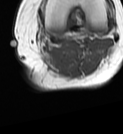
MRI of an extremity soft-tissue mass, one axial slice; position 51 of 68 along the scan axis; MR volume resampled by the dataset authors to the PET/CT grid (not the native acquisition matrix); 123 × 134 image matrix. Female patient. Case-level facts recorded for this patient, not image findings: histological type: extraskeletal high grade osteogenic sarcoma; grade: high; site of the primary tumour: left calf.
Outlined on this slice (expert contour drawn on MRI and transferred to this co-registered scan by the dataset authors):
- gross tumour volume (mass): bounding box <47,46,66,65> (left, top, right, bottom; pixels)